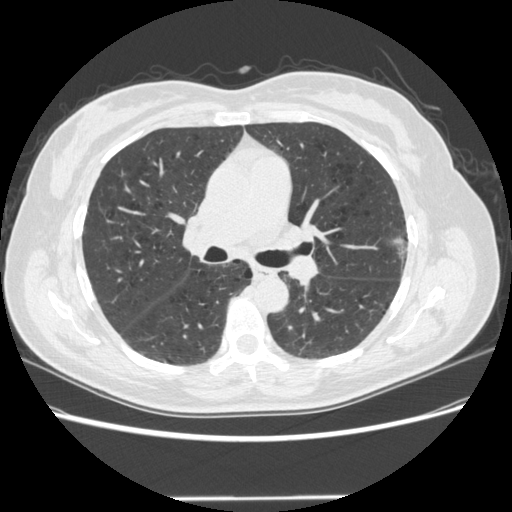
Chest CT (low-dose screening protocol), one axial image, baseline annual screen, lung window (W 1500 / L -600 HU), 1.25 mm slice thickness, slice 187 of 301 in the series, 512 × 512 image matrix, field of view 360 × 360 mm. Female, age 61 years at enrolment.
- Expert reader's lesion annotation, box from (x=383, y=227) to (x=427, y=277) px.
- Screening reader's record for this exam: no non-calcified nodule ≥4 mm recorded.
- Official screen result: negative screen, minor abnormalities not suspicious for lung cancer.